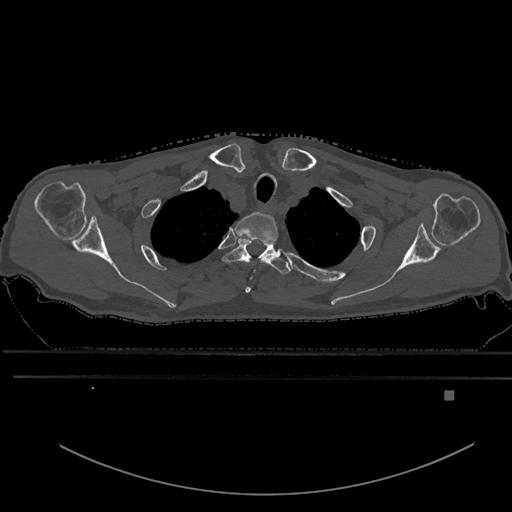
CT including the spine, one axial slice; slice 509 of 969 in the series (ordered by position); bone window (W 1800 / L 400 HU); 0.5 mm slice thickness; 512 × 512 image matrix, field of view 456 × 456 mm. Patient: male, 82 years. Case-level facts recorded for this patient, not image findings: primary cancer: prostate; vertebrae with lytic lesions (as recorded): T11, T9, T8, T2.
Structures marked on this image (semi-automatic segmentation, software-assisted and operator-edited):
- T1 vertebra: bounding box (x1, y1, x2, y2) in pixels: (234, 212, 279, 293)
- T2 vertebra: (222, 239, 291, 275)